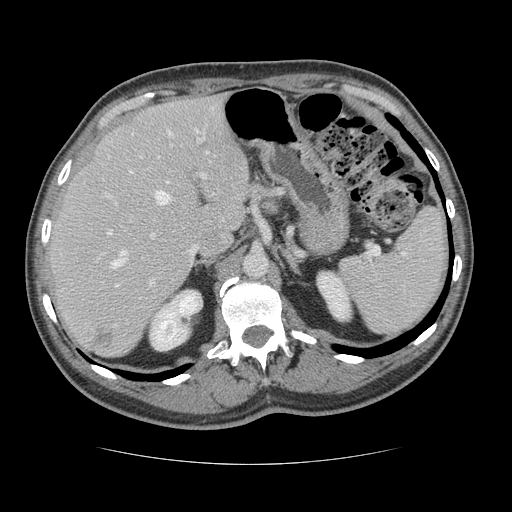
Contrast-enhanced abdominal CT, one axial slice; position 87 of 134 along the scan axis; intravenous contrast given; soft-tissue window (W 400 / L 40 HU); 2.5 mm slice thickness; 512 × 512 image matrix, field of view 377 × 377 mm. Male patient, age 68 years. From the clinical record (not read from this slice): diagnosis: colorectal cancer liver metastases, imaged before liver resection; multiple liver metastases: yes; largest metastasis: 2.2 cm; chemotherapy before resection: no.
Annotated regions visible in this slice (manually delineated by an expert):
- hepatic veins: bounding box [x1, y1, x2, y2] px = [112, 131, 213, 267]
- liver: [49, 97, 250, 356]
- planned liver remnant (the part of the liver to remain after resection): [49, 97, 250, 337]
- portal vein (with intrahepatic branches): [108, 129, 207, 285]
- liver metastasis: [95, 328, 114, 348]